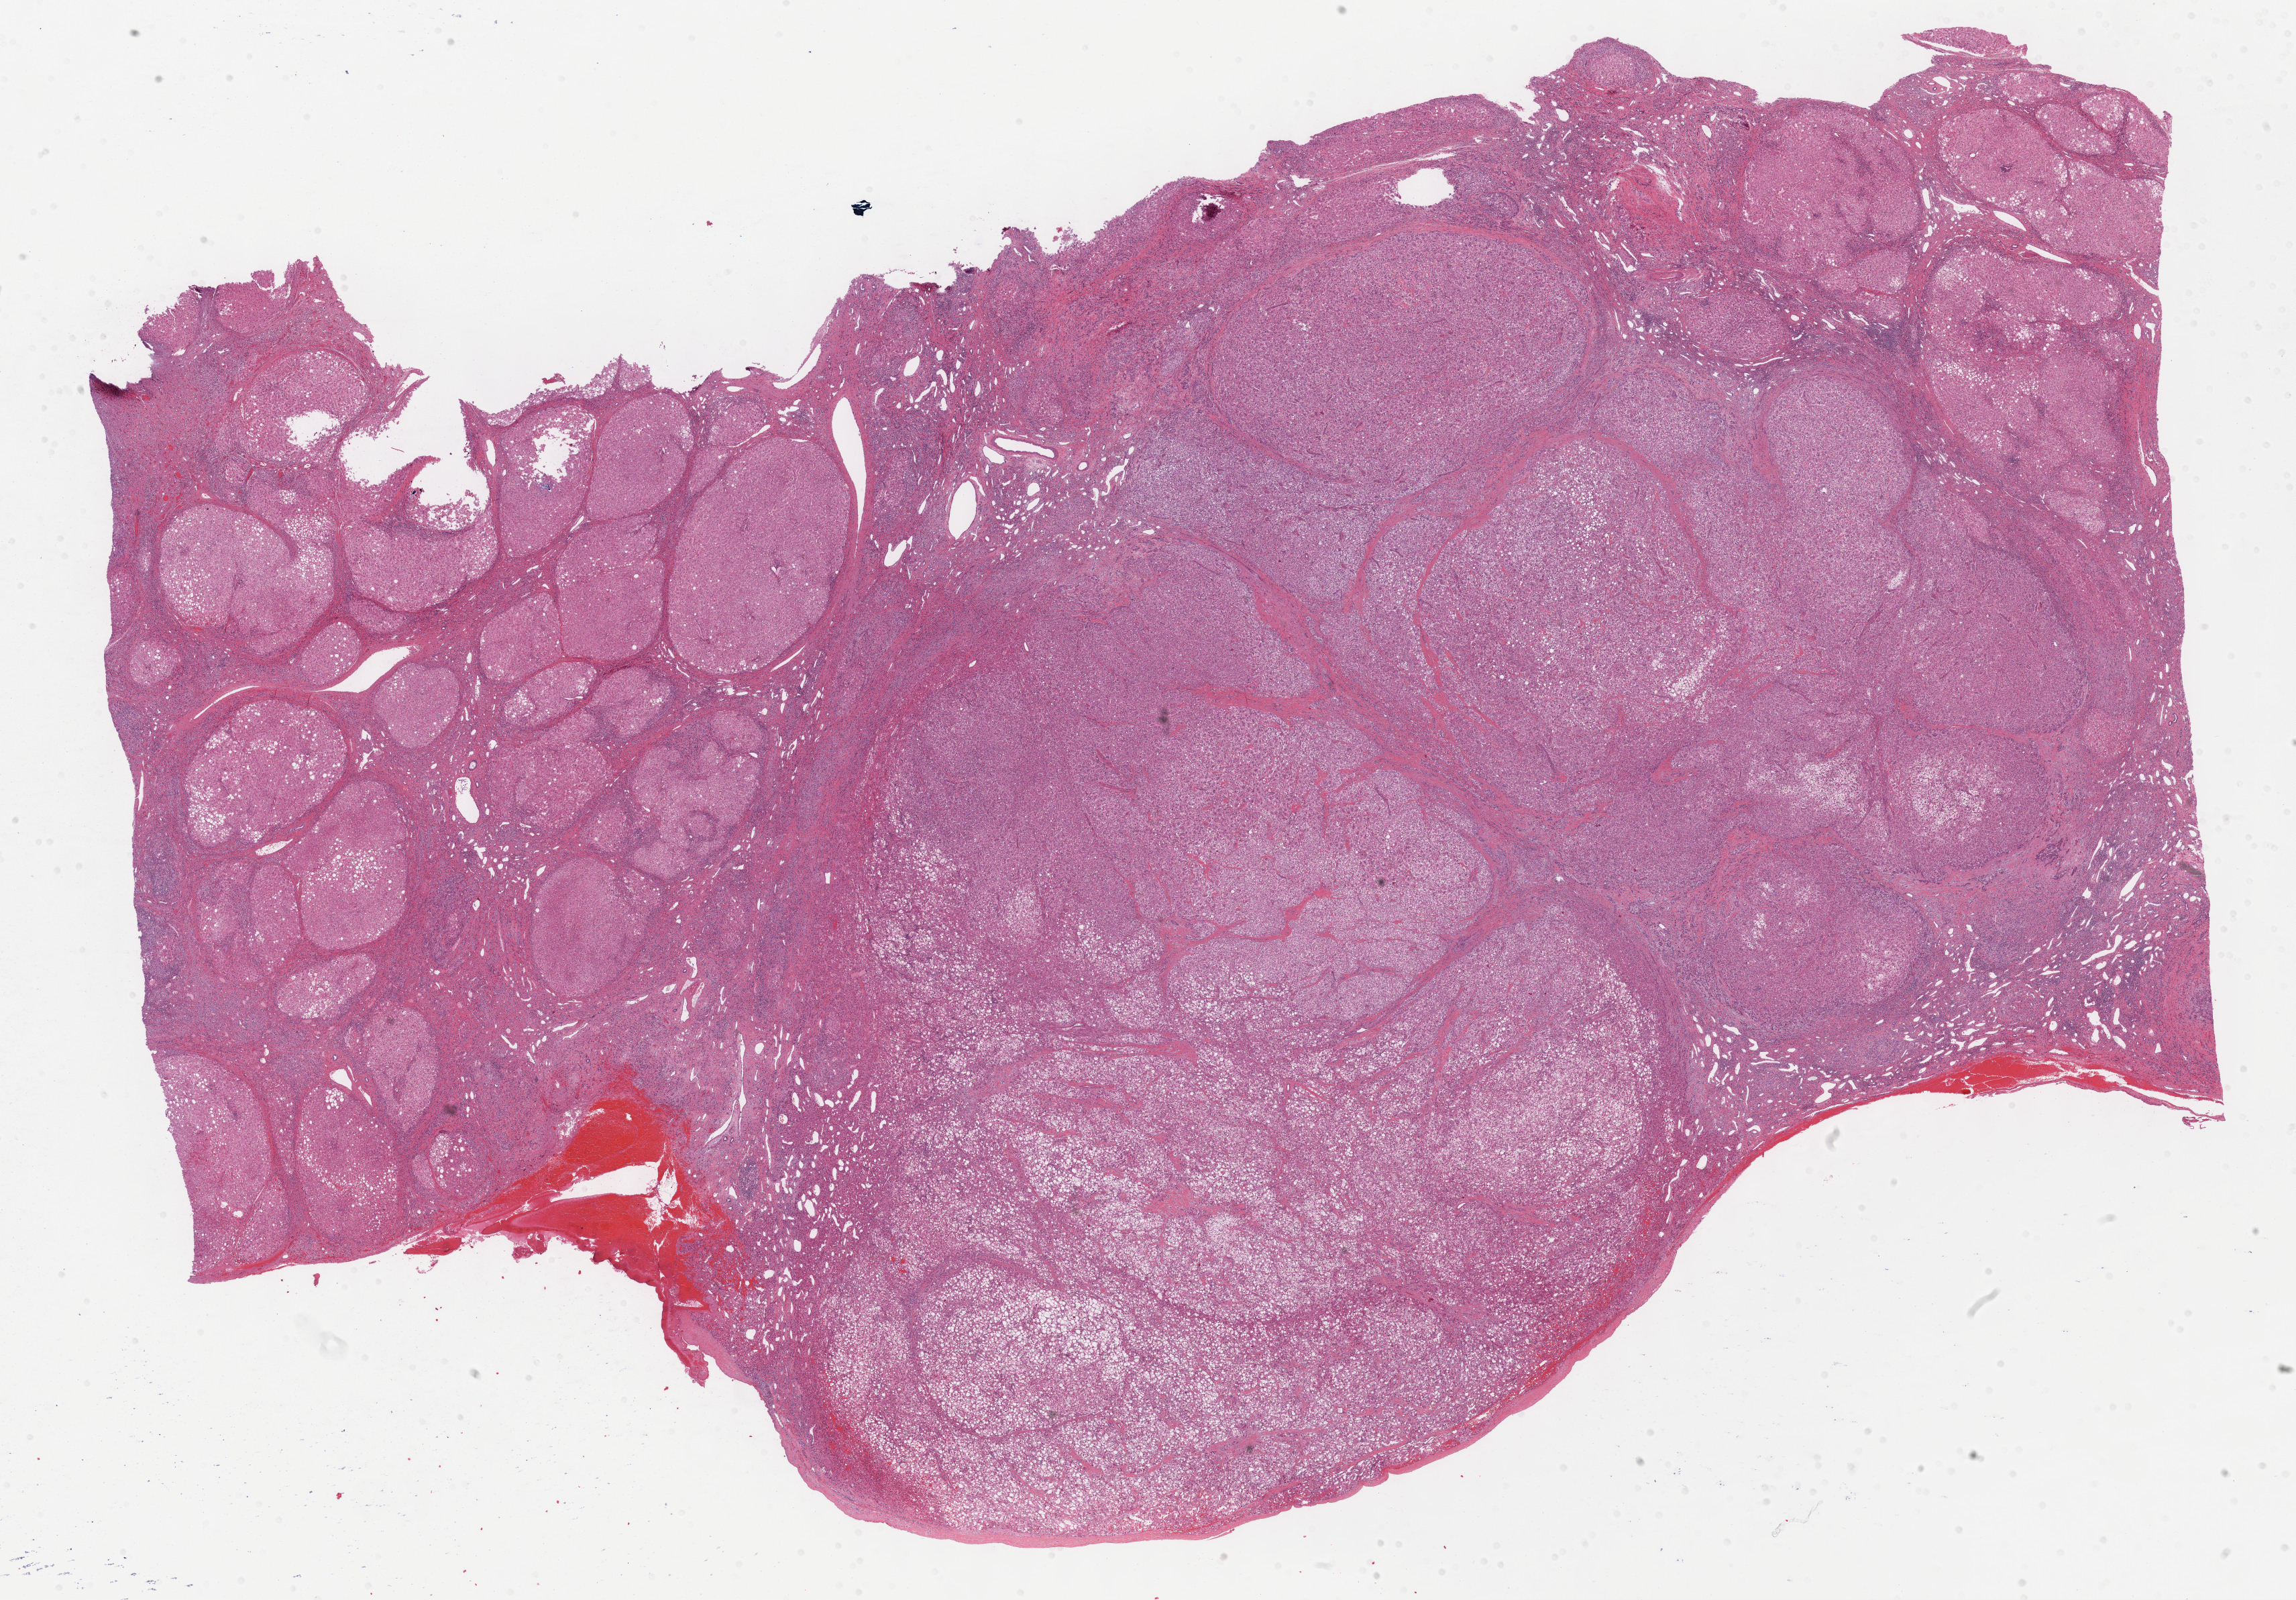
Whole-slide histology image, H&E-stained, shown as a low-resolution overview of the whole scanned area (about 27.7 x 19.3 mm, acquisition: 40x scan); formalin-fixed paraffin-embedded (FFPE) diagnostic section; liver, primary tumour sample. Patient: female, age at initial diagnosis 56 years. Histologic grade: G2 (moderately differentiated).
- pathologic diagnosis: Hepatocellular carcinoma, NOS